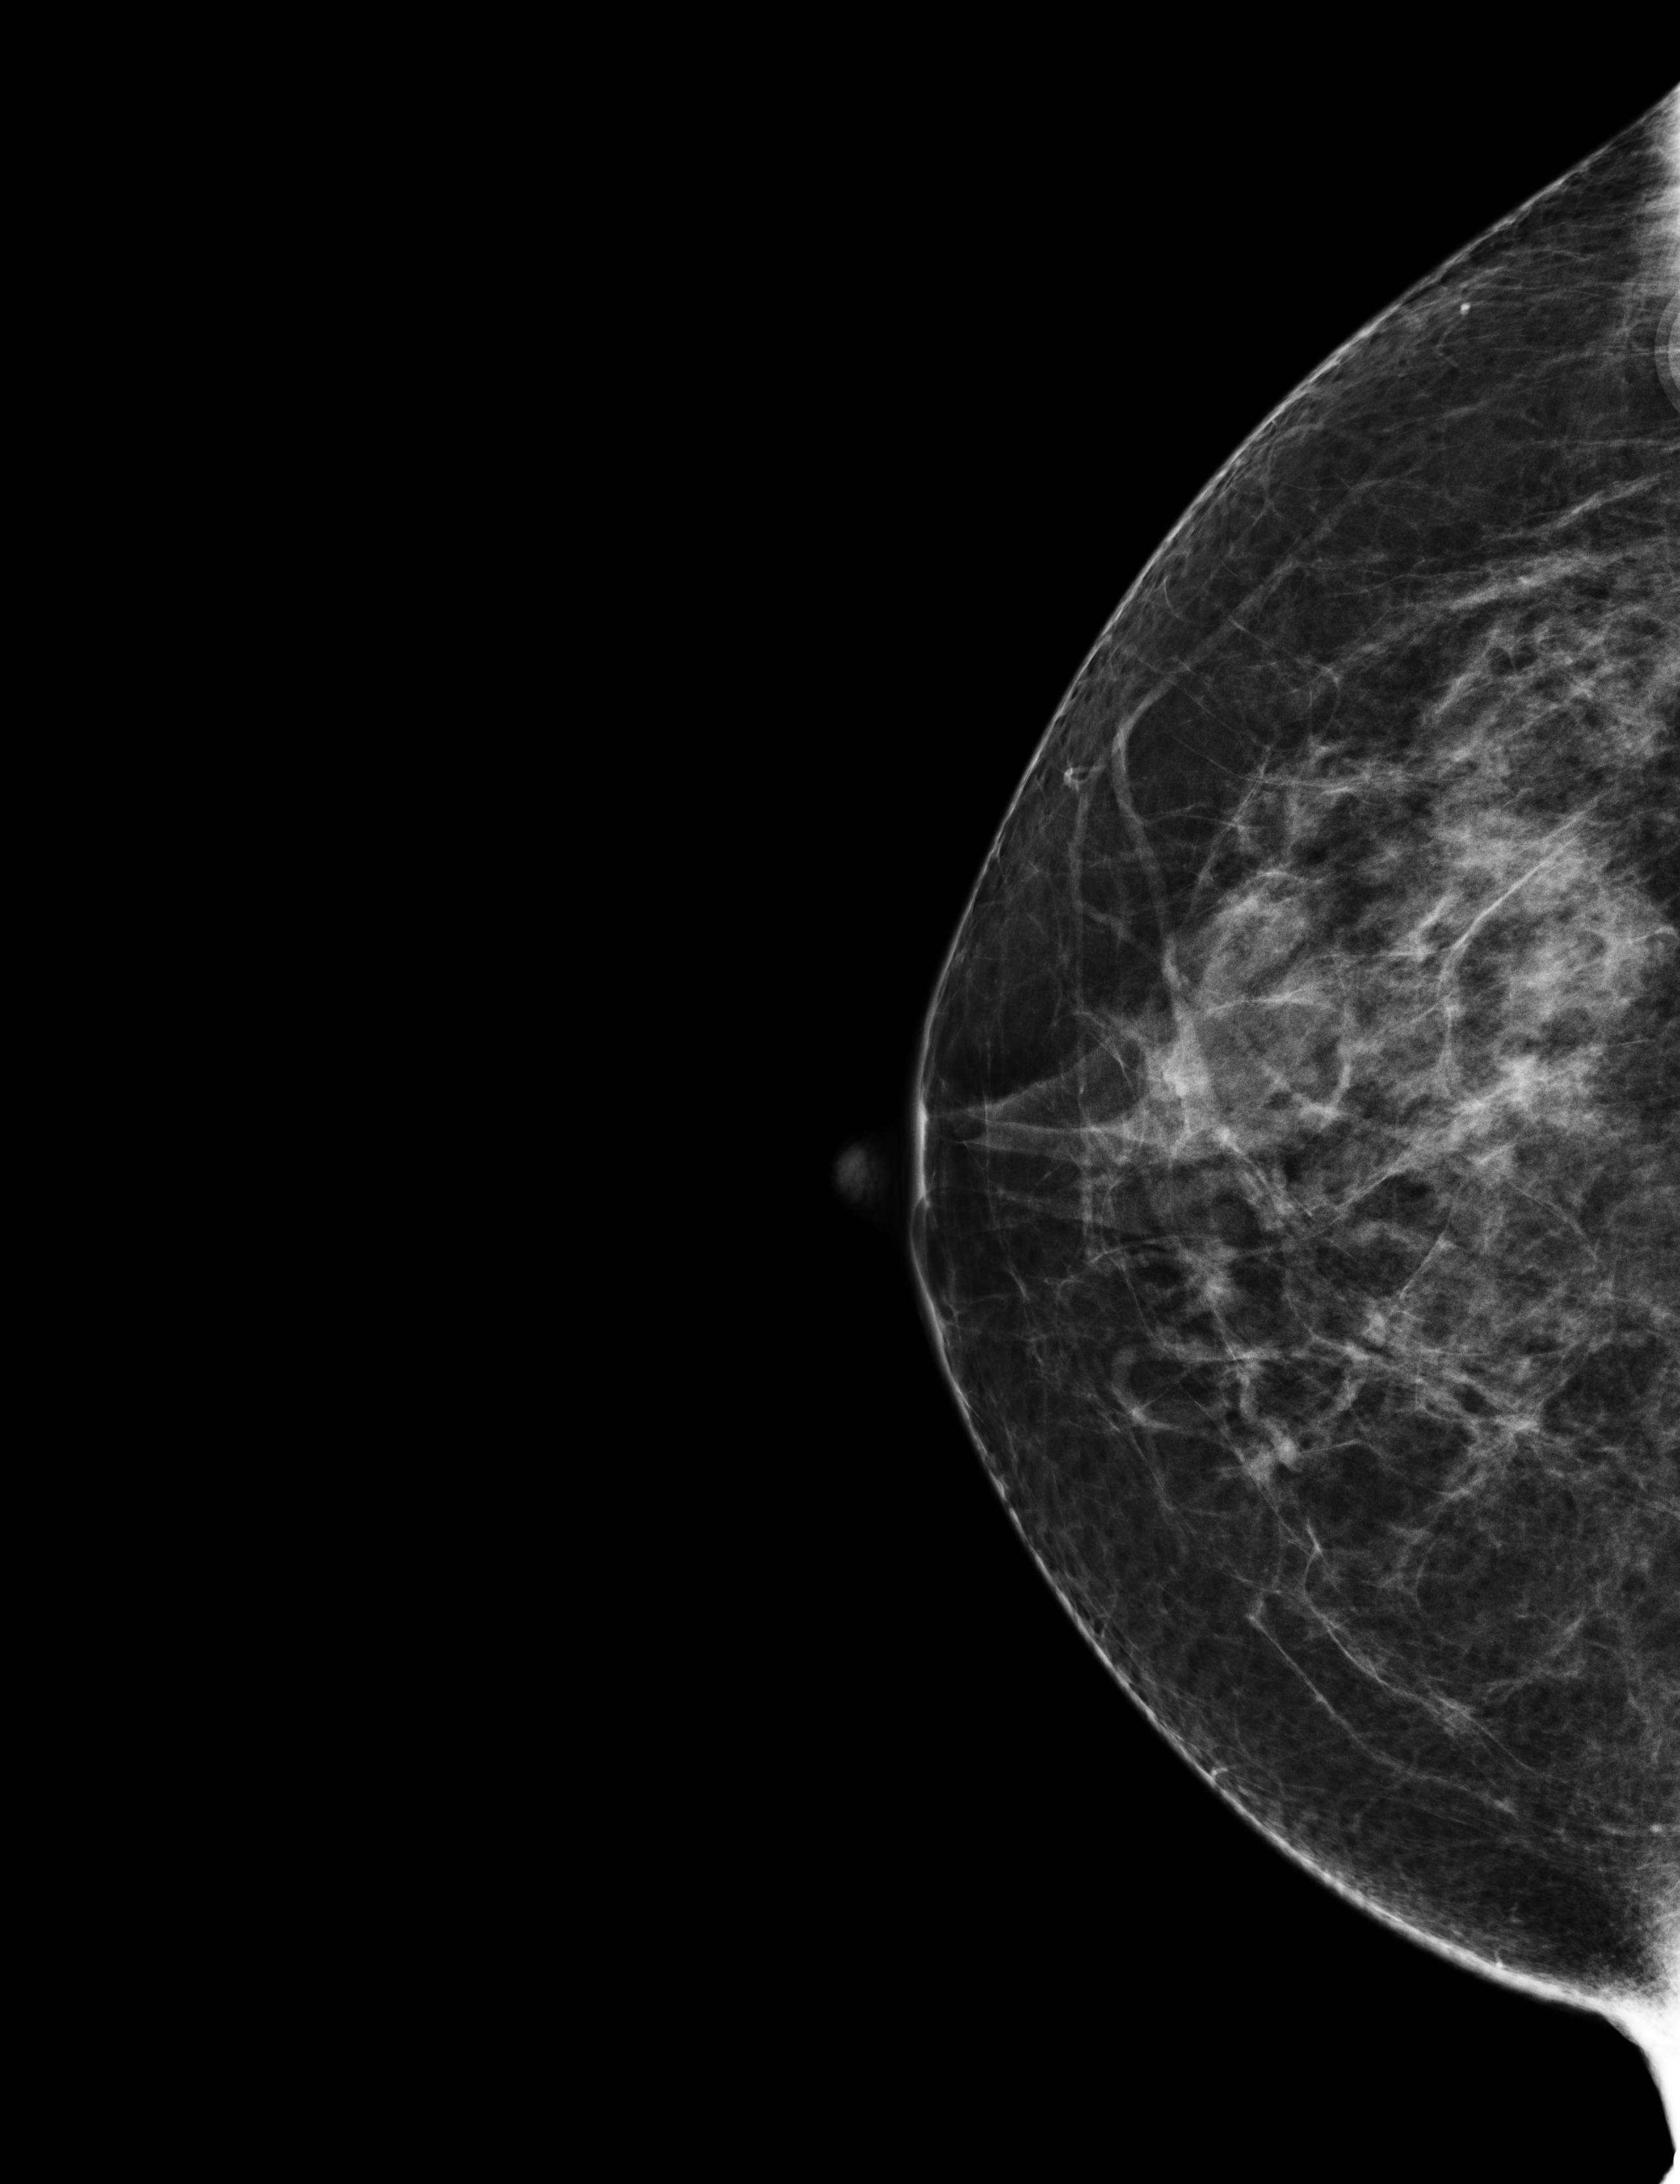
Annual screening mammography examination; compressed breast thickness 74 mm. Patient: female, 54 years.
Image type: full-field digital mammogram. Breast: right. Projection: CC view.